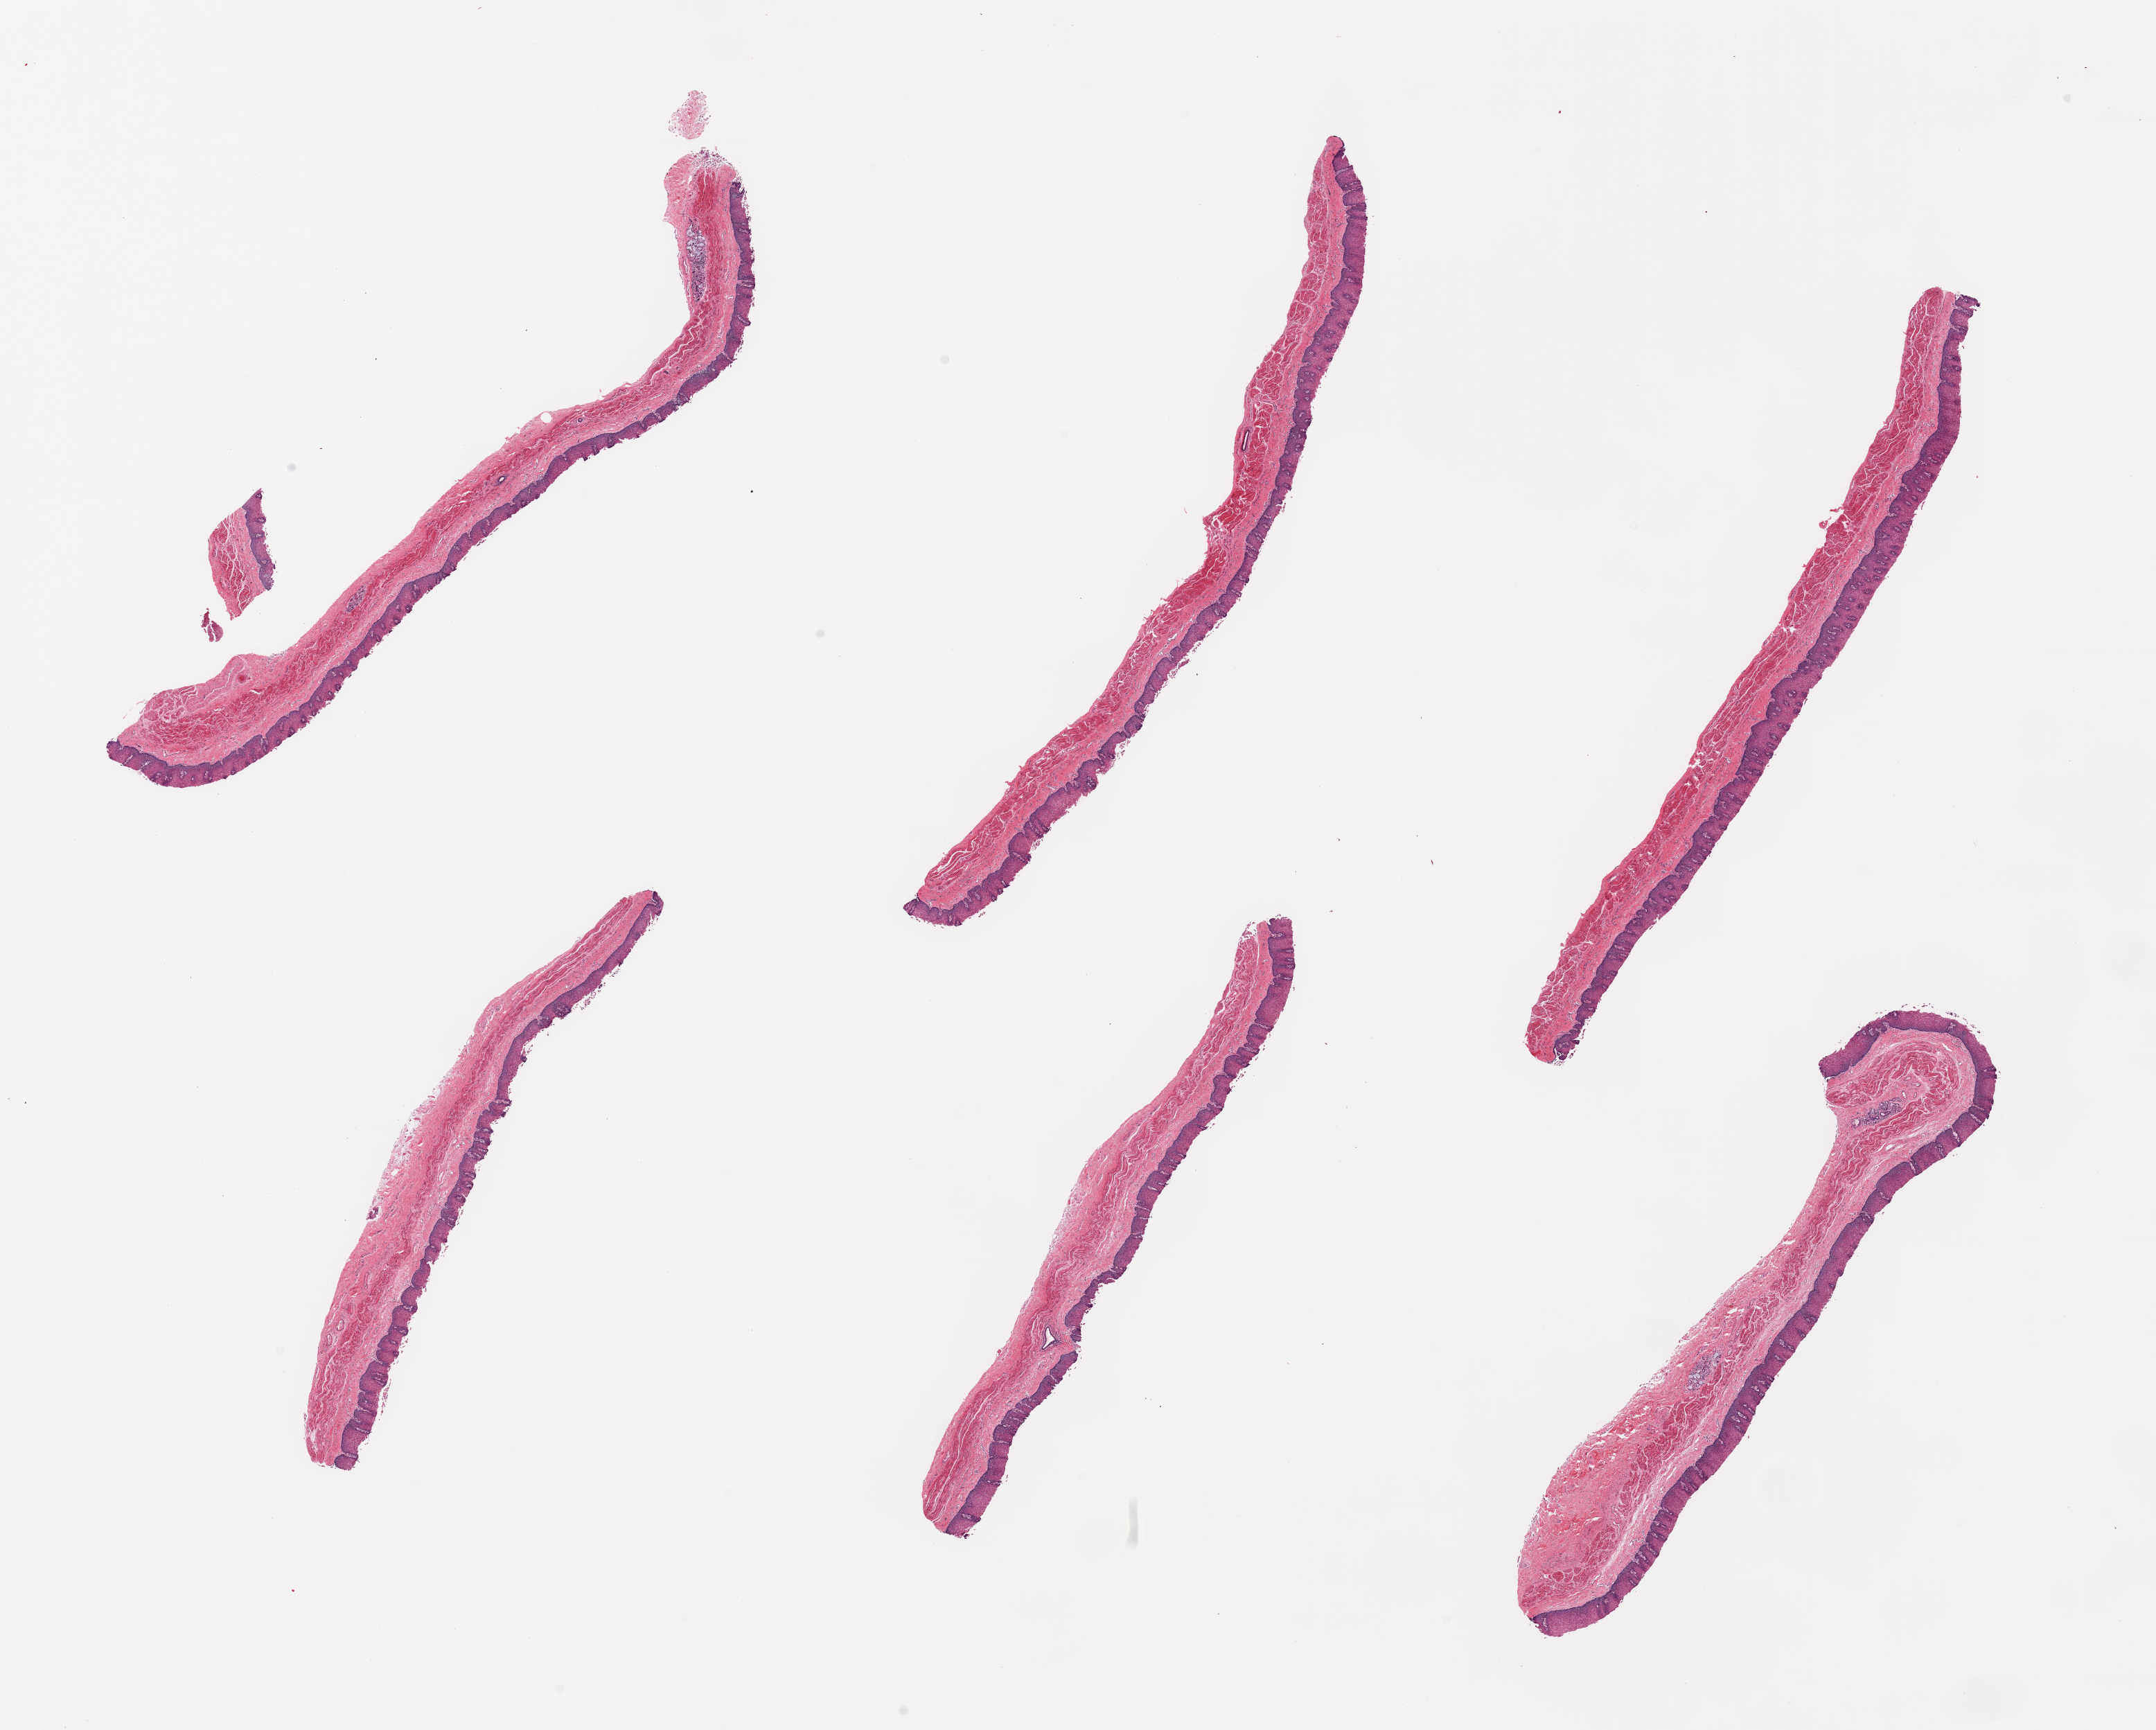
Digitized H&E-stained section, brightfield, a low-resolution overview of the entire scanned area, about 24.6 x 19.7 mm, PAXgene-fixed paraffin-embedded (PFPE) section, sampled site (target tissue): esophageal mucous membrane, tissue donor sample. Donor sex: female.
Review note (as recorded): 6 pieces; partially sloughed superficial epithelium; well dissected.